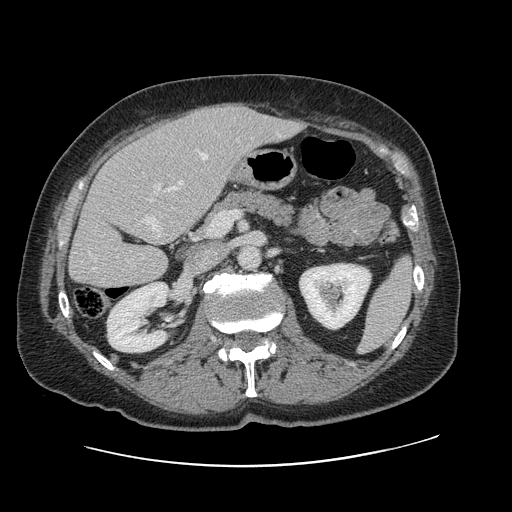
Contrast-enhanced abdominal CT, one axial slice; slice 48 of 138 in the series (ordered by position); 120 kVp; intravenous contrast given; soft-tissue window (W 400 / L 40 HU); 2.5 mm slice thickness; 512 × 512 image matrix, field of view 402 × 402 mm. Male patient, age 71 years. From the clinical record (not read from this slice): diagnosis: colorectal cancer liver metastases, imaged before liver resection; multiple liver metastases: no; largest metastasis: 3.3 cm; chemotherapy before resection: no.
Structures marked on this image (outlined manually by an expert reader):
- hepatic veins: box from (x=89, y=153) to (x=208, y=270) px
- liver: (x=70, y=105)–(x=299, y=289)
- planned liver remnant (the part of the liver to remain after resection): (x=70, y=139)–(x=197, y=289)
- portal vein (with intrahepatic branches): (x=150, y=184)–(x=161, y=202)